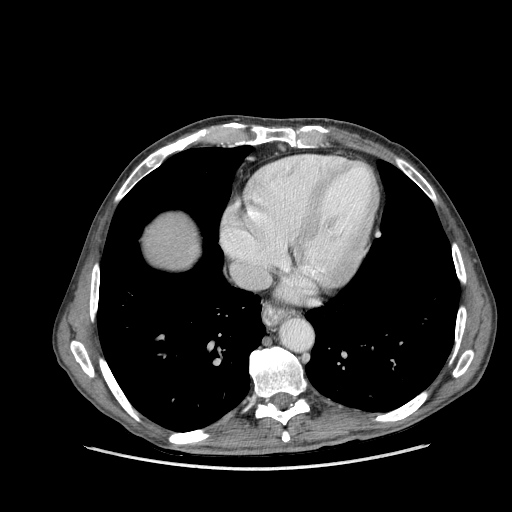
Contrast-enhanced abdominal CT (liver protocol), one axial slice. Position 145 of 162 along the scan axis. Reconstruction kernel STANDARD. 100 kVp. Soft-tissue window (W 400 / L 40 HU). 2.5 mm slice thickness. 512 × 512 image matrix, field of view 400 × 400 mm. Case-level facts recorded for this patient, not image findings: diagnosis: hepatocellular carcinoma (patient treated with transarterial chemoembolisation; whether this scan precedes or follows treatment is not stated here); TNM stage (as recorded): Stage-IIIA; Child-Pugh class: A; tumour size: 9.9 cm.
Structures marked on this image (semi-automatic segmentation, software-assisted and operator-edited):
- liver parenchyma outside the tumour (the mass and vessels are separate outlines, so this box may not span the whole liver): bounding box (x1, y1, x2, y2) in pixels: (146, 214, 198, 268)